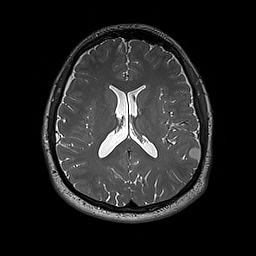
Brain MRI from a brain-tumour surgery series, one axial slice; slice 87 of 192 in the series (ordered by position); 1 mm slice thickness; 256 × 256 image matrix, field of view 250 × 250 mm. Case-level facts recorded for this patient, not image findings: histopathology: Dysembryoplastic neuroepithelial tumor; WHO grade: 1; IDH mutation: no; tumour location: Left Inferior Parietal.
Structures marked on this image (manually delineated by an expert):
- tumour: bounding box <189,148,201,161> (left, top, right, bottom; pixels)